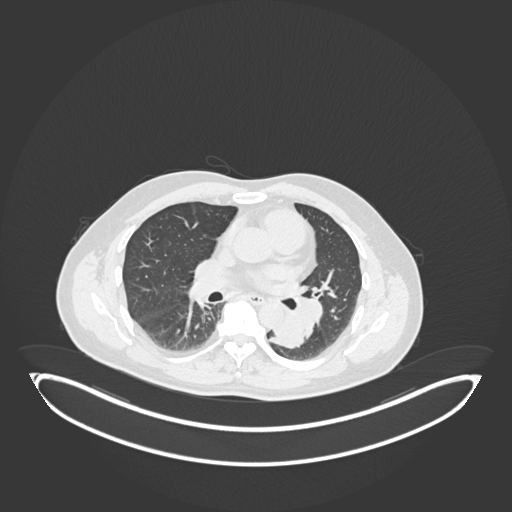
Chest CT, one axial slice. Slice 107 of 258 in the series (ordered by position). Reconstruction kernel B30f. 120 kVp. Lung window (W 1500 / L -600 HU). 1 mm slice thickness. 512 × 512 image matrix, field of view 500 × 500 mm. Male patient, age 54 years. From the clinical record (not read from this slice): clinical TNM (as recorded): T3 N0 M0.
Structures marked on this image (bounding box drawn by a radiologist):
- lung tumour (recorded histology: squamous cell carcinoma): bounding box <269,312,306,353> (left, top, right, bottom; pixels)